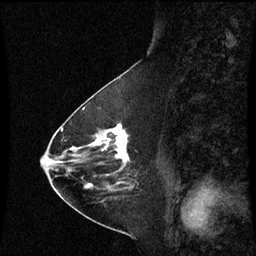
Breast MRI (dynamic contrast-enhanced), one sagittal slice; position 27 of 60 along the scan axis; dynamic contrast-enhanced series, image 2 of 3 at this slice position (ordered by acquisition); 1.5 T; TE 4.2 ms, TR 8.9 ms; 2 mm slice thickness; 256 × 256 image matrix. Patient: female, 63 years. From the clinical record (not read from this slice): setting: breast cancer imaged before/during neoadjuvant chemotherapy; receptor status: HR-positive, HER2-negative.
Annotated regions visible in this slice (semi-automatic segmentation, software-assisted and operator-edited):
- analysis volume of interest (the breast-tissue region the enhancement analysis was run in; not a lesion): bounding box [x1, y1, x2, y2] px = [94, 122, 131, 177]
- tumour enhancement mask (voxels above the 70 % enhancement threshold inside the analysis volume of interest): [96, 124, 130, 161]